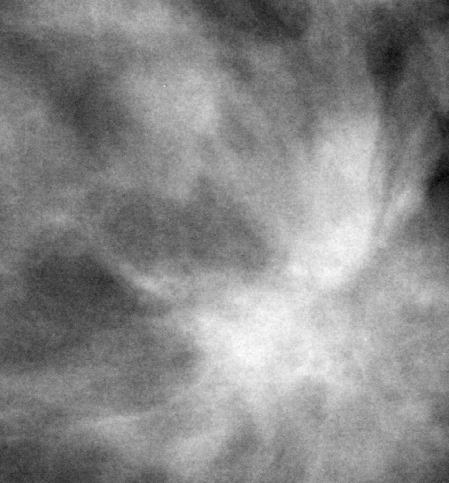
Crop from a digitized film mammogram around one marked abnormality; left breast; CC view.
Mass, shape irregular, margins spiculated; BI-RADS assessment category 5; pathology result (as recorded, not read from the image): malignant.